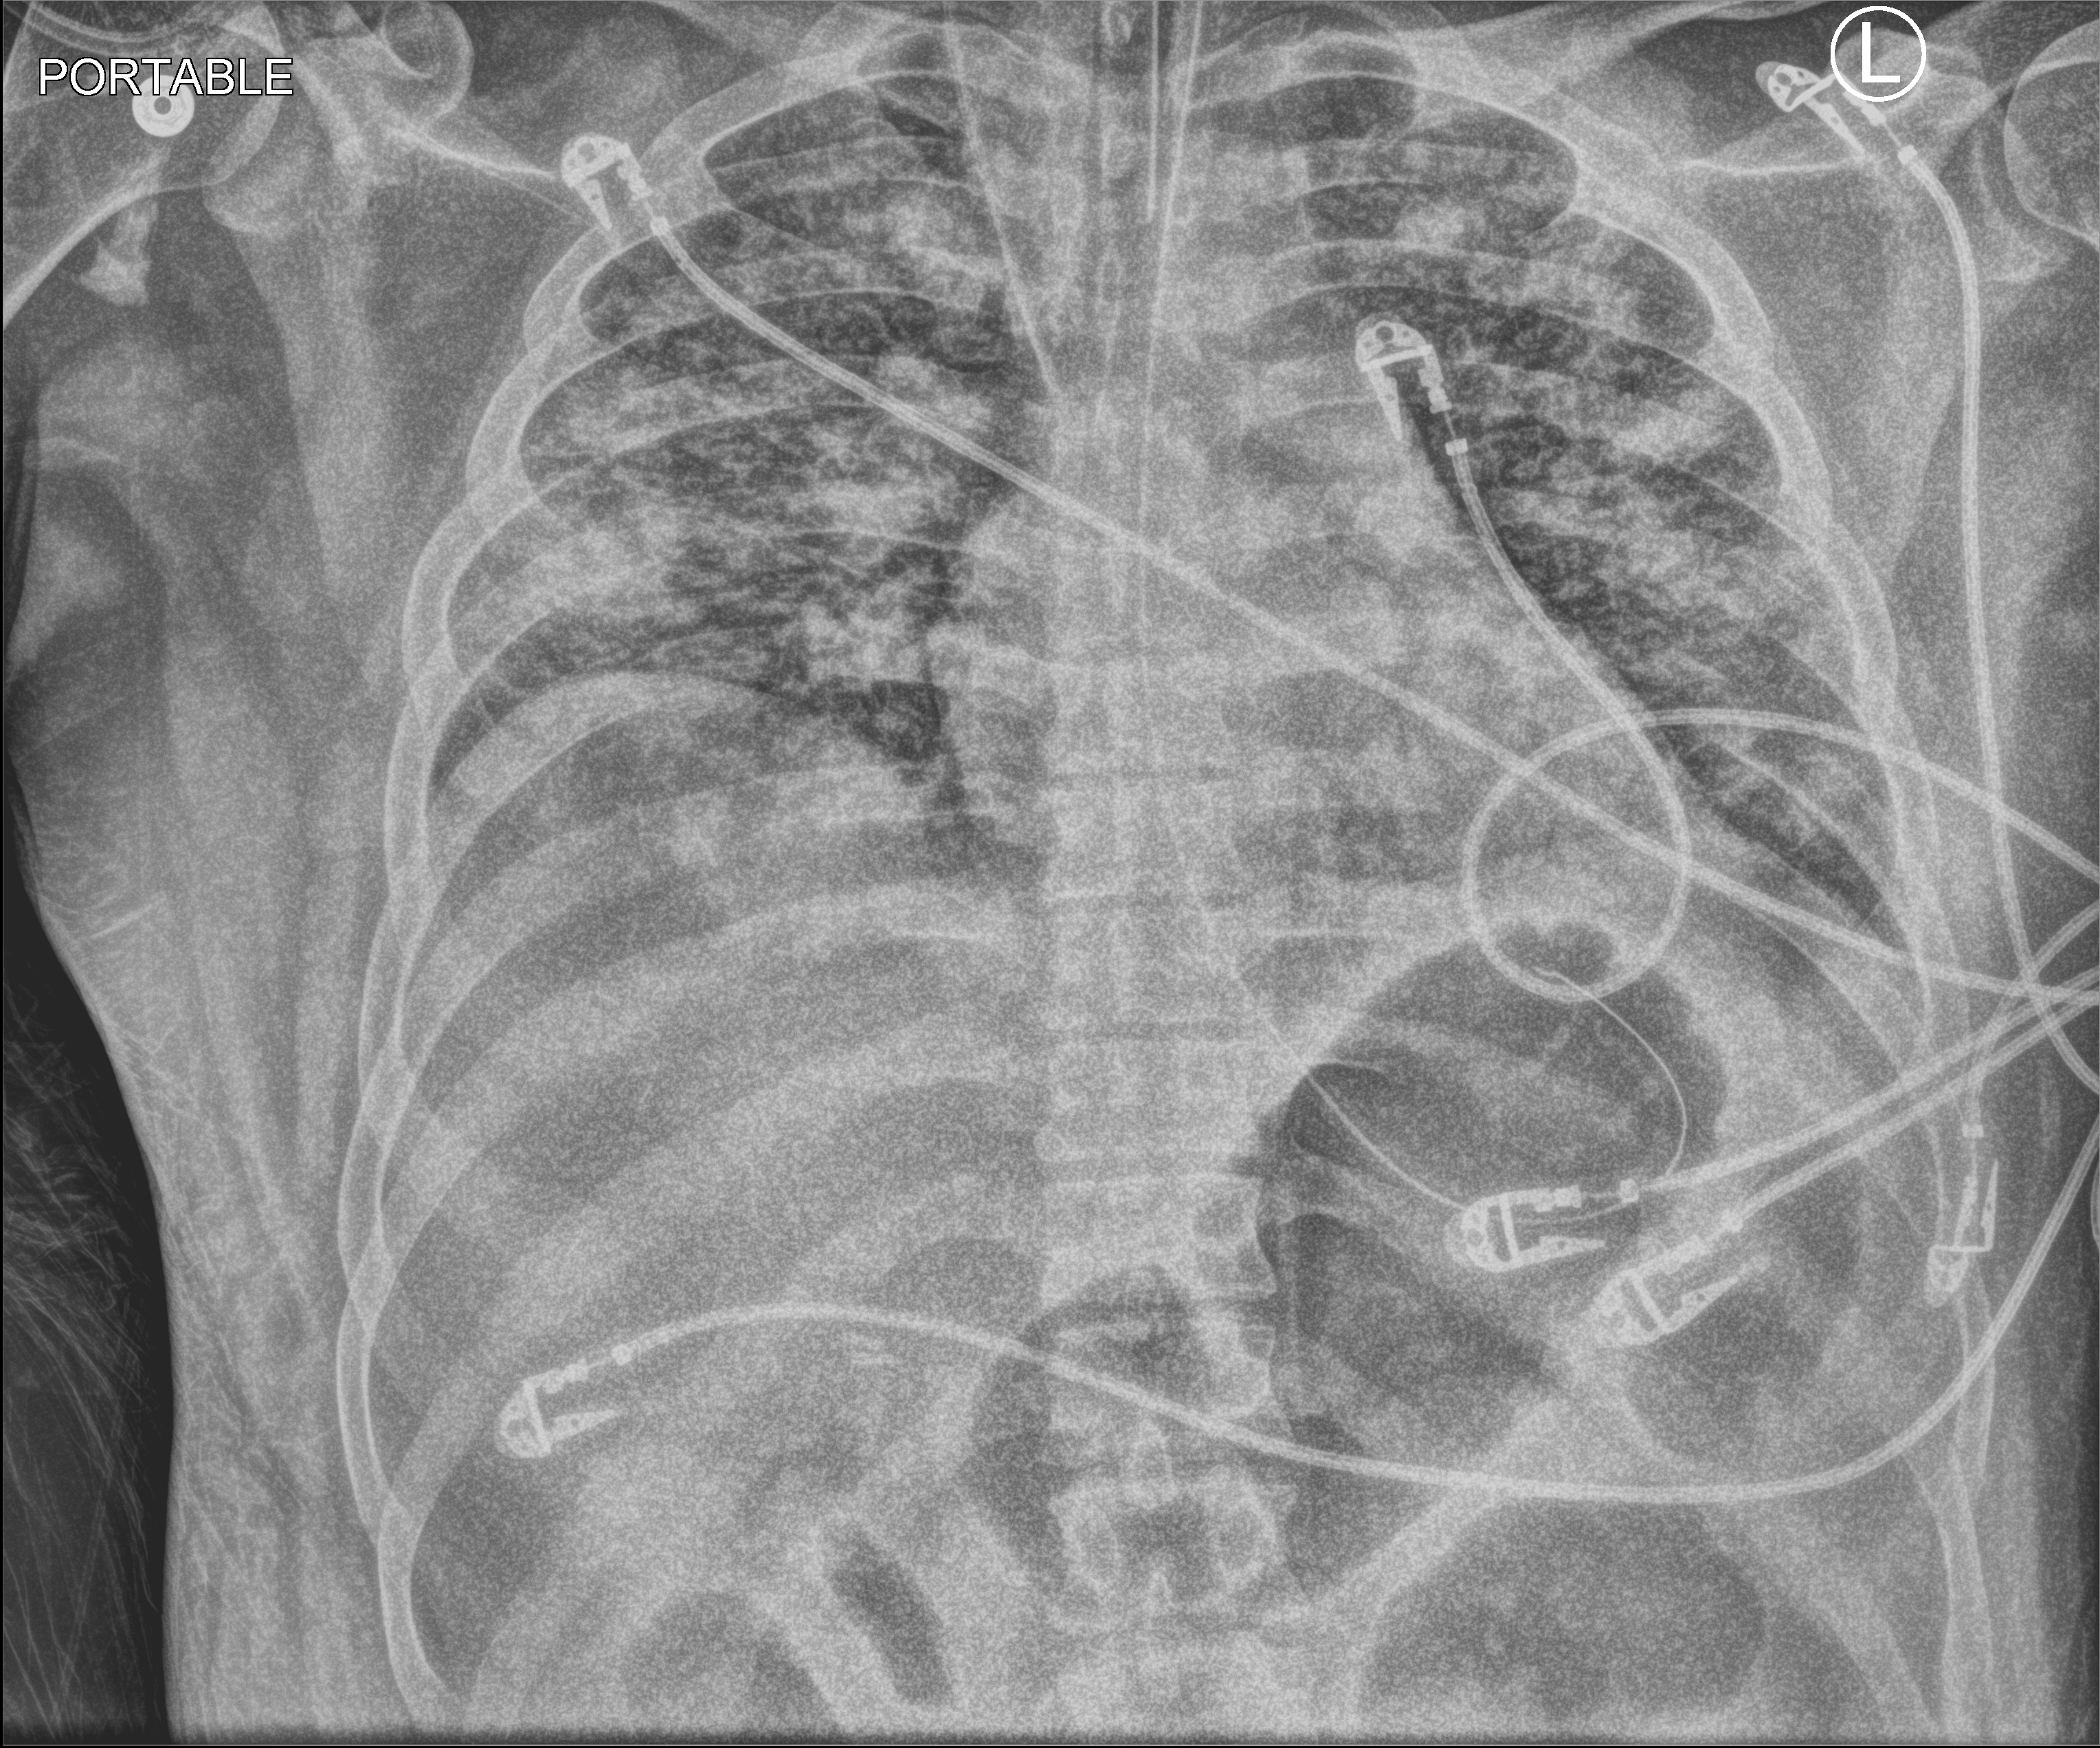
Bedside chest radiograph (computed radiography); anteroposterior (AP) projection. Male patient hospitalised with COVID-19, age 18–59 years.
Admission-level facts for this patient (not findings on this image; timing relative to this image not recorded): chronic kidney disease (admission record): no; COPD (admission record): no.